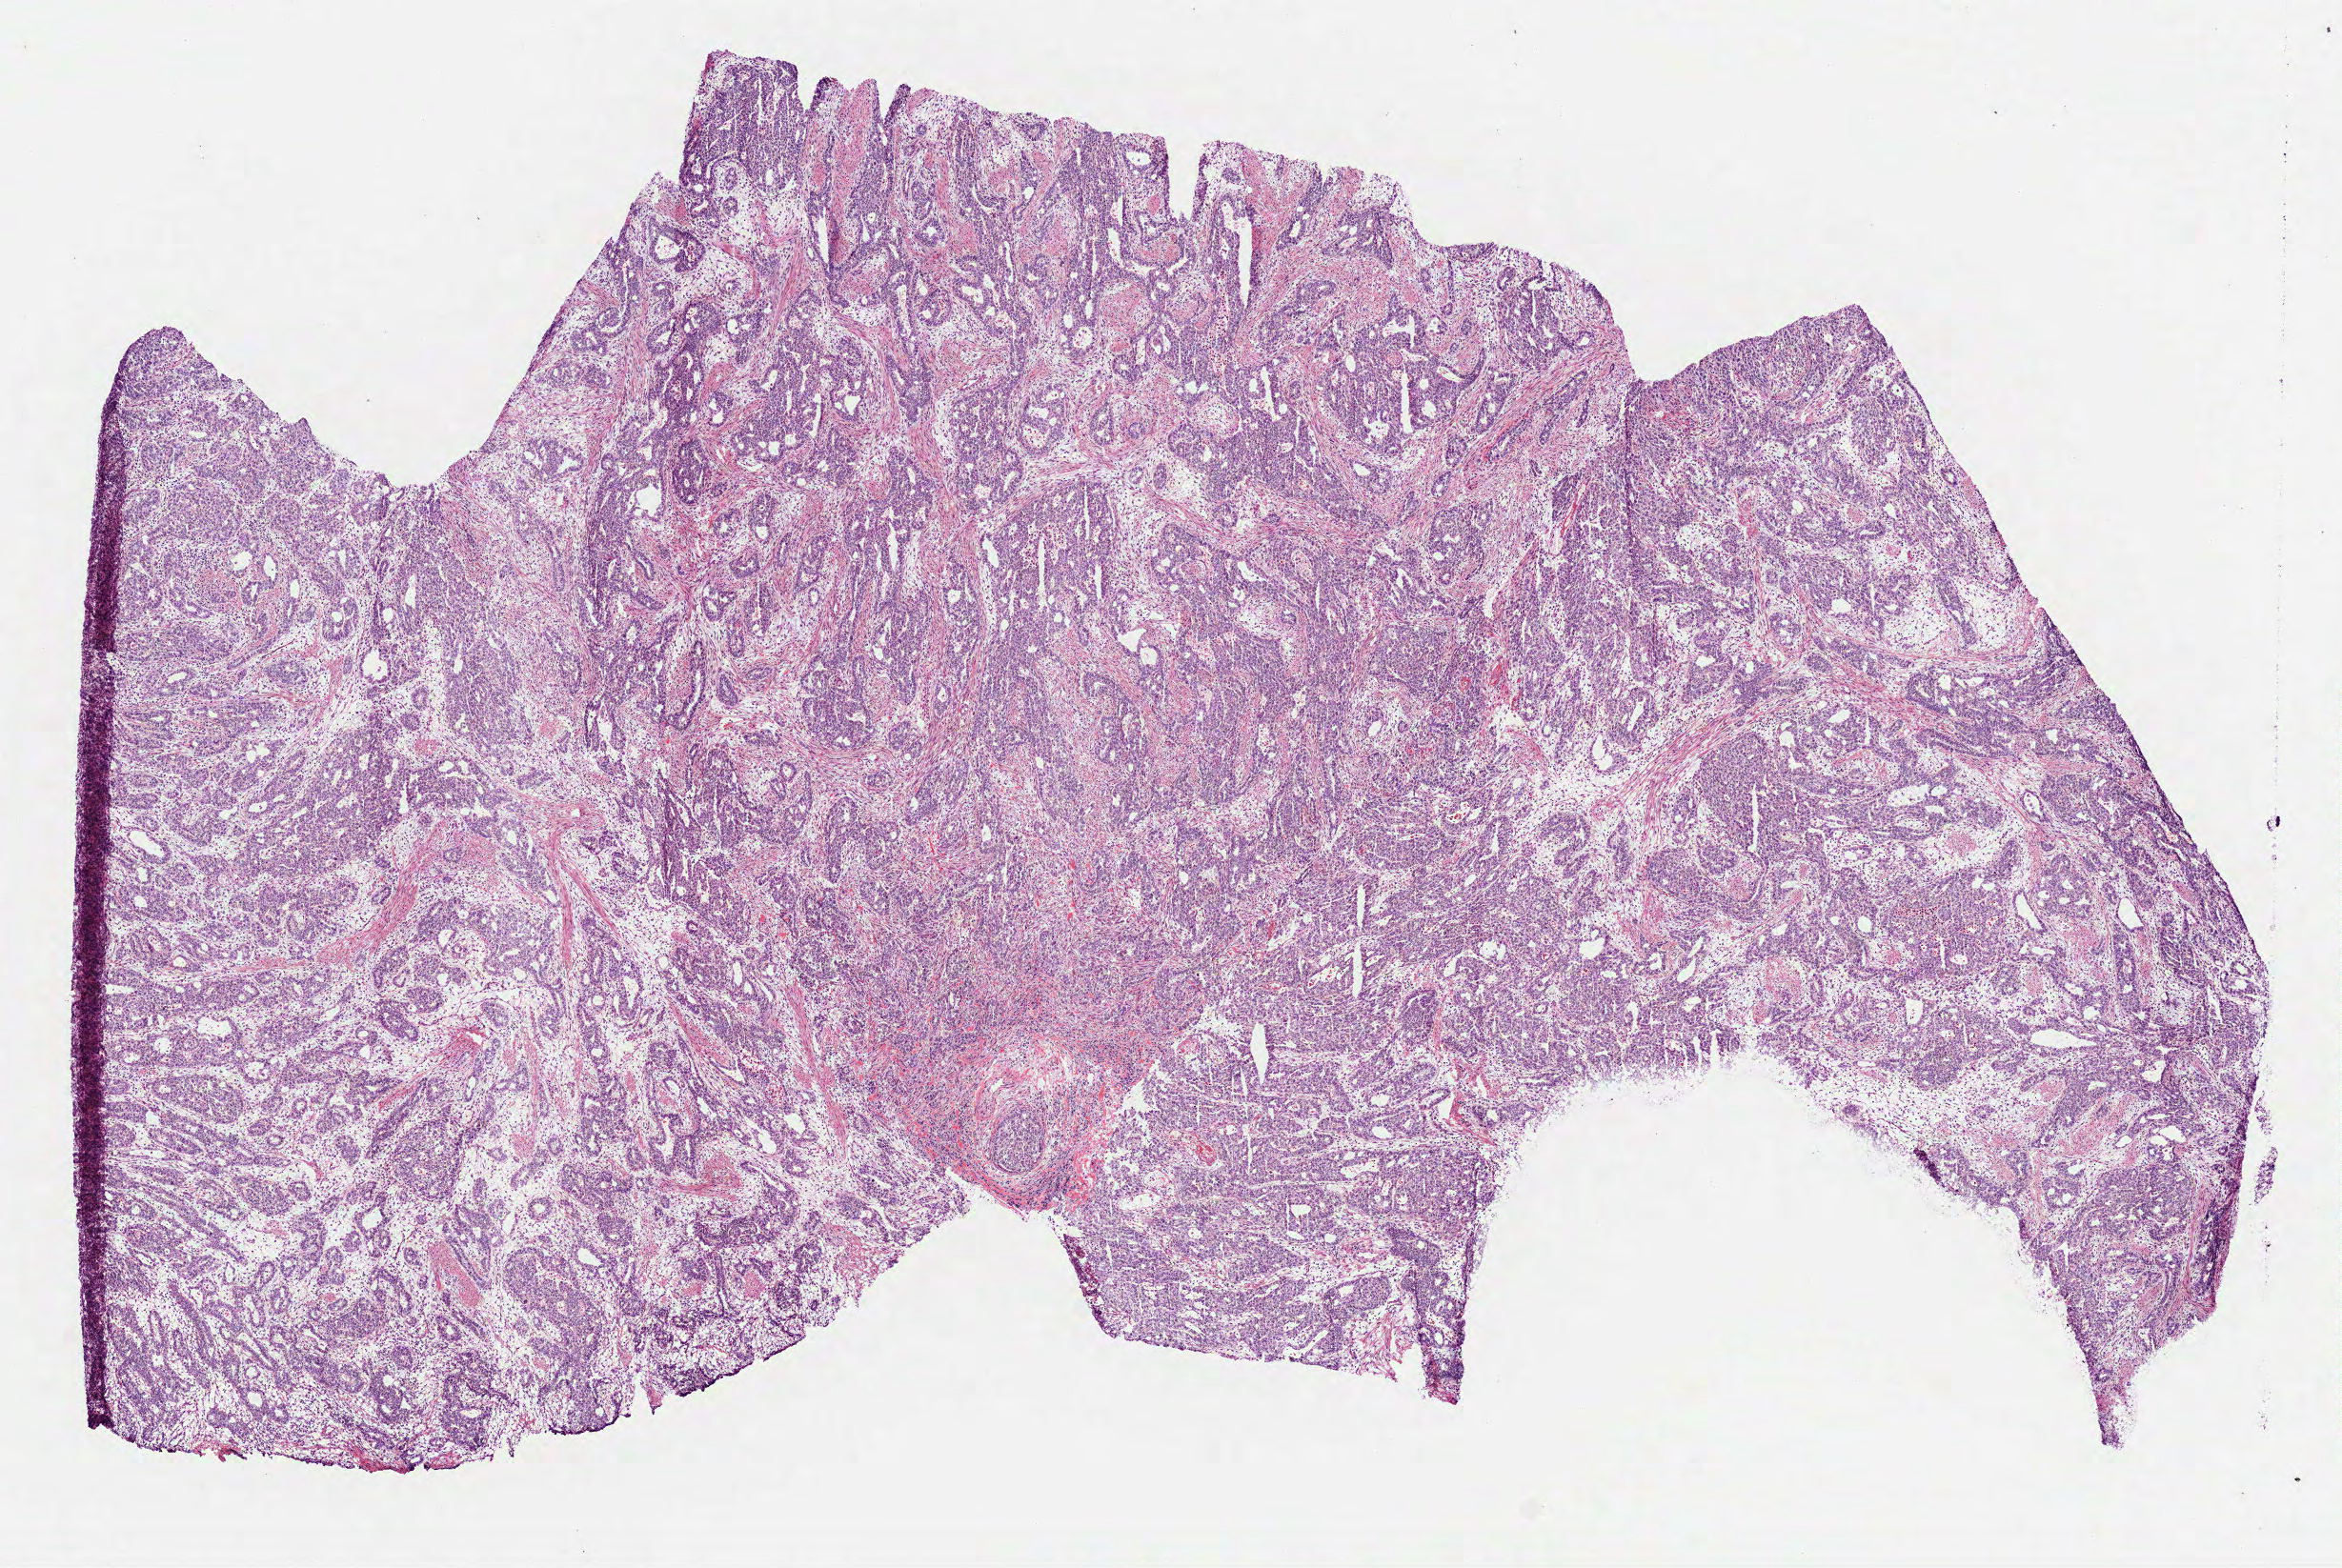
Digitized H&E-stained tissue section (whole slide) — whole scanned area (about 9.9 x 6.6 mm, acquisition: 40x scan) shown as a low-resolution overview. Frozen section from the bottom of the tissue portion. Primary tumour sample from the stomach. Patient sex: male. Histologic grade: G2 (moderately differentiated). Composition of this section per pathologist review: tumour cells 99%, tumour nuclei 70%, normal cells 0%, stromal cells 0%, necrosis 1%. Inflammatory infiltration, as recorded: lymphocyte infiltration 11%, monocyte infiltration 2%, neutrophil infiltration 5%.
- AJCC pathologic stage: IIIA
- histologic diagnosis: Adenocarcinoma, NOS (cardia, NOS)
- TNM: T3 N1 M0